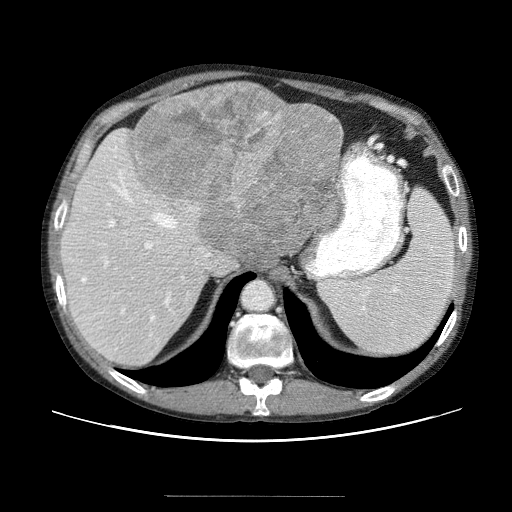
Contrast-enhanced abdominal CT (liver protocol), one axial slice. Position 40 of 69 along the scan axis. Reconstruction kernel STANDARD. 120 kVp. Soft-tissue window (W 400 / L 40 HU). 2.5 mm slice thickness. 512 × 512 image matrix, field of view 380 × 380 mm. From the clinical record (not read from this slice): diagnosis: hepatocellular carcinoma (patient treated with transarterial chemoembolisation; whether this scan precedes or follows treatment is not stated here); TNM stage (as recorded): Stage-IVB; Child-Pugh class: B; tumour differentiation: poorly differentiated; tumour nodularity: multinodular.
Structures marked on this image (semi-automatic segmentation, software-assisted and operator-edited):
- liver parenchyma outside the tumour (the mass and vessels are separate outlines, so this box may not span the whole liver): bounding box (x1, y1, x2, y2) in pixels: (58, 105, 342, 370)
- mass: (129, 80, 342, 260)
- liver vessels: (79, 155, 213, 329)